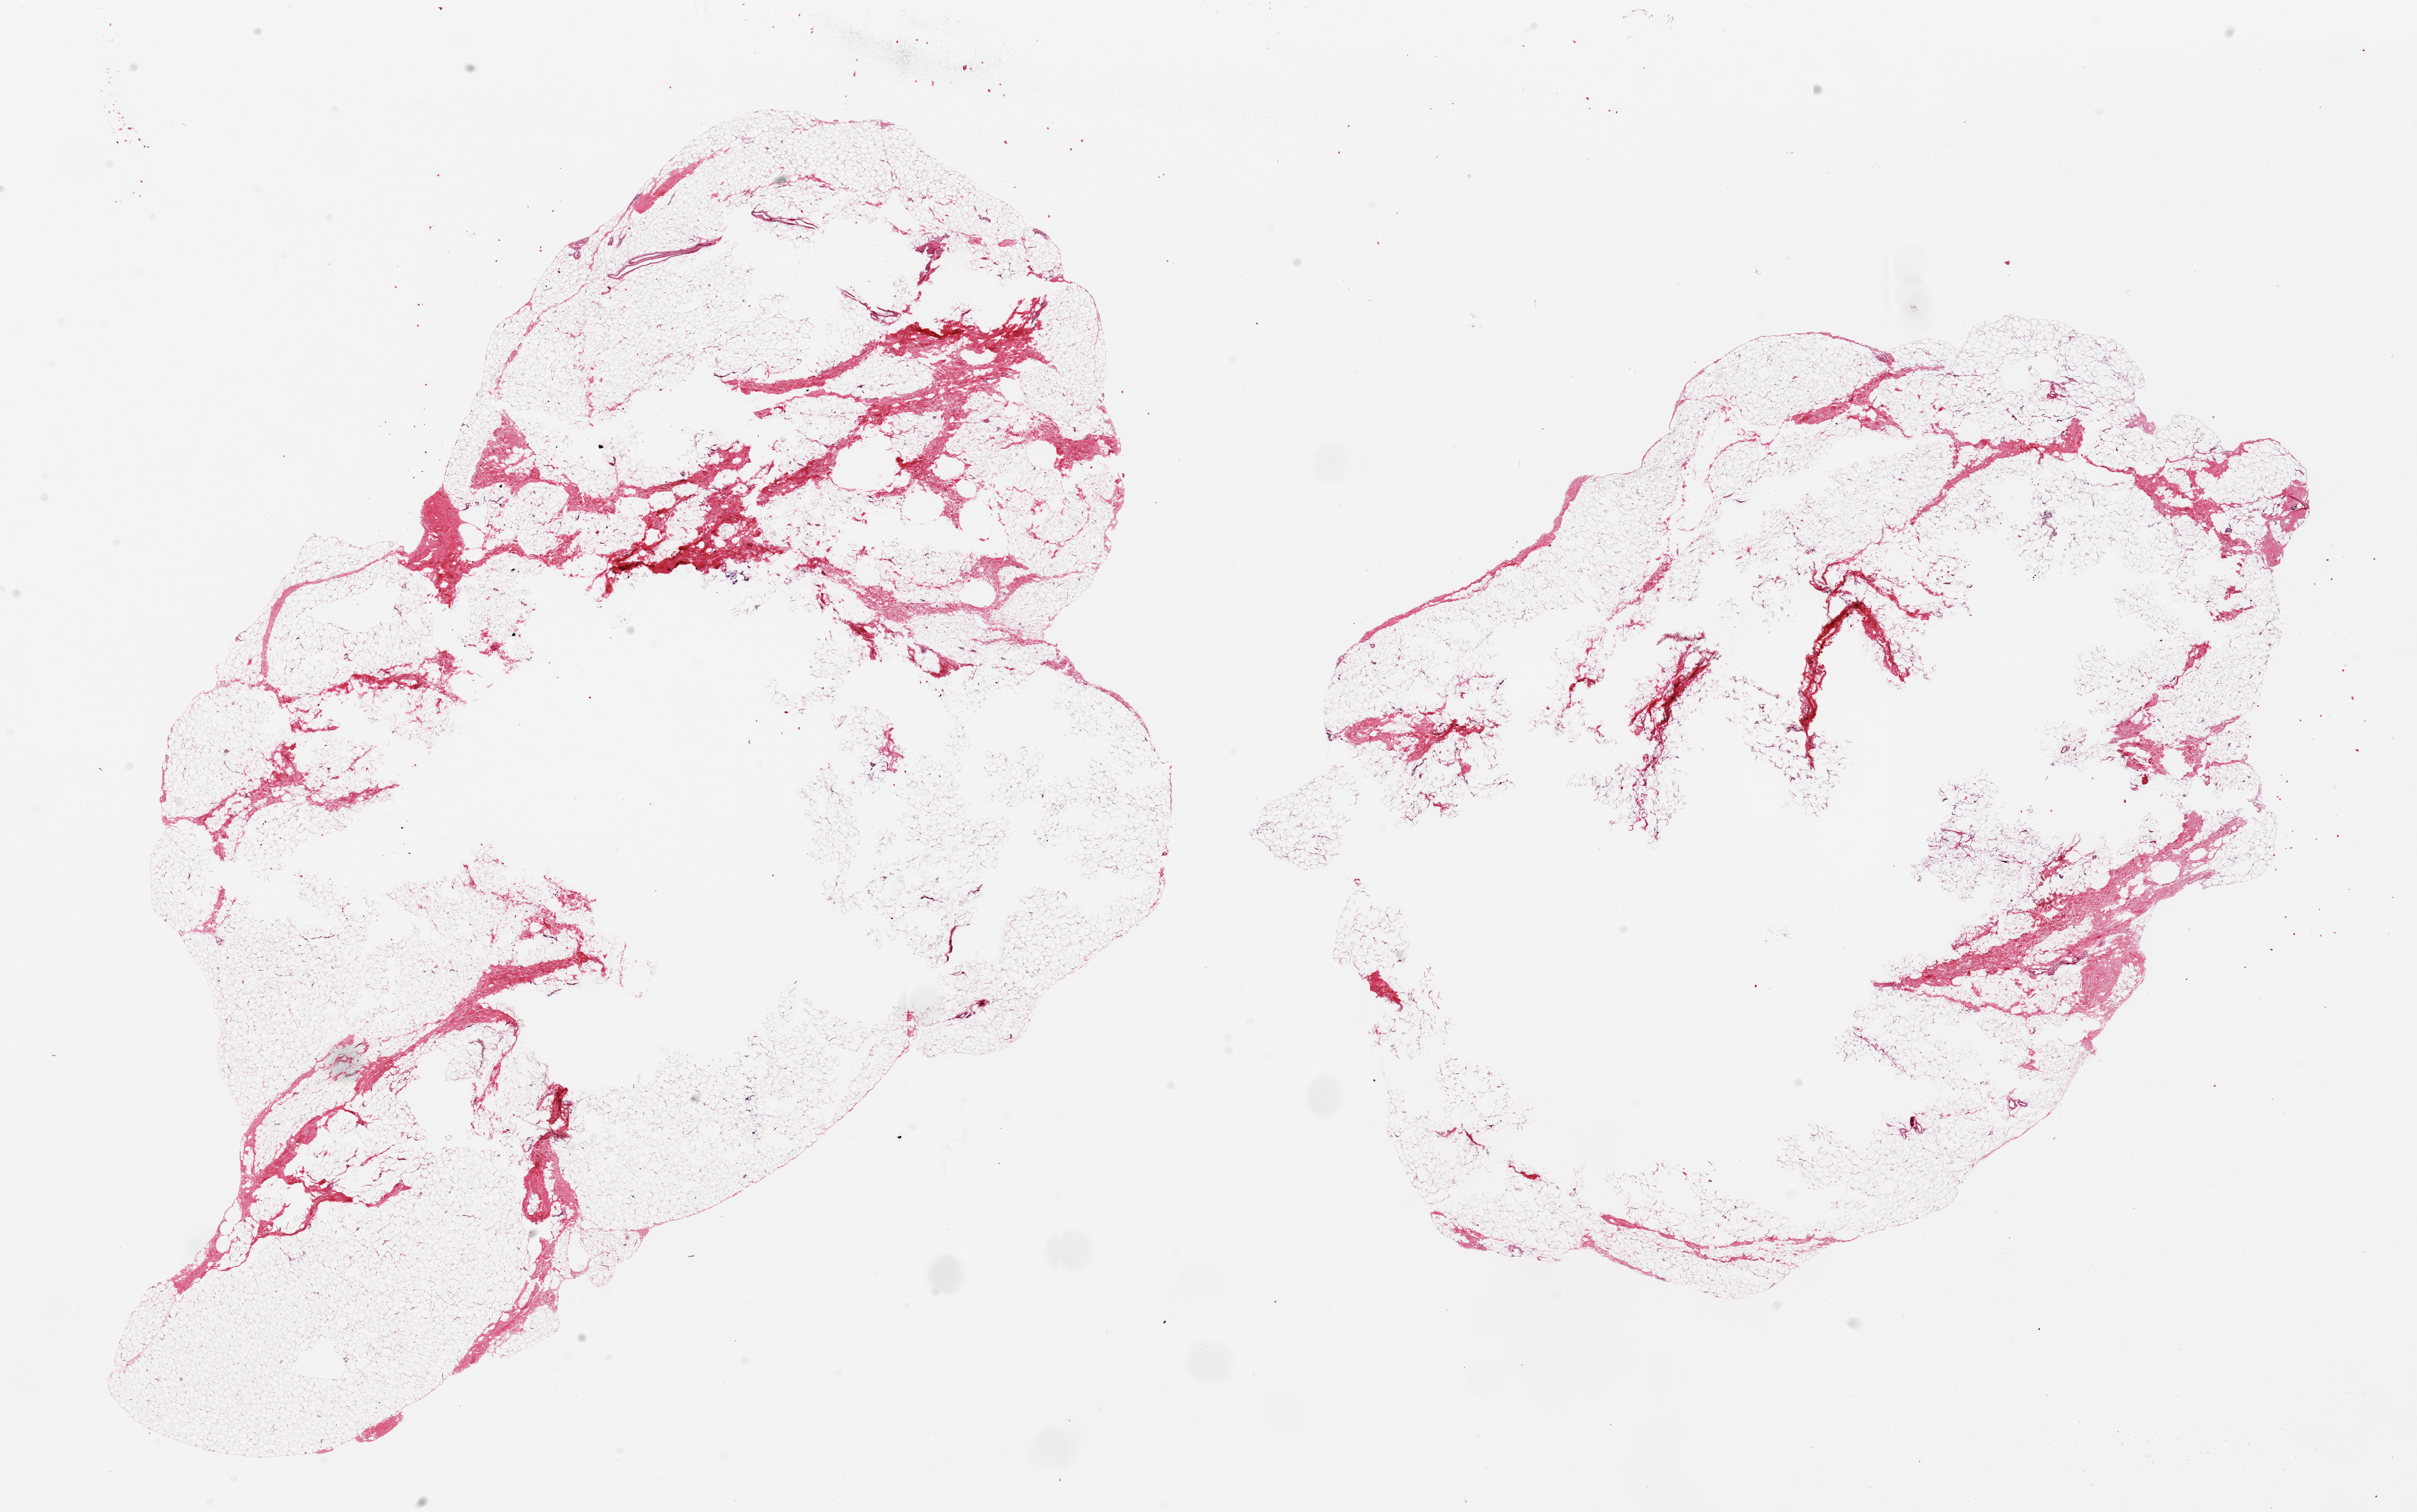
Whole-slide image, haematoxylin and eosin stain — whole scanned area (about 31.5 x 19.7 mm, acquisition: 20x scan) shown as a low-resolution overview. PAXgene-fixed paraffin-embedded (PFPE) section. Target tissue: breast. Donor tissue sample. Donor sex: male.
* pathologist's review note for this sample: 2 pieces, 18x12 & 14x11.5mm; all fibradipose tissue, no ductal elements seen